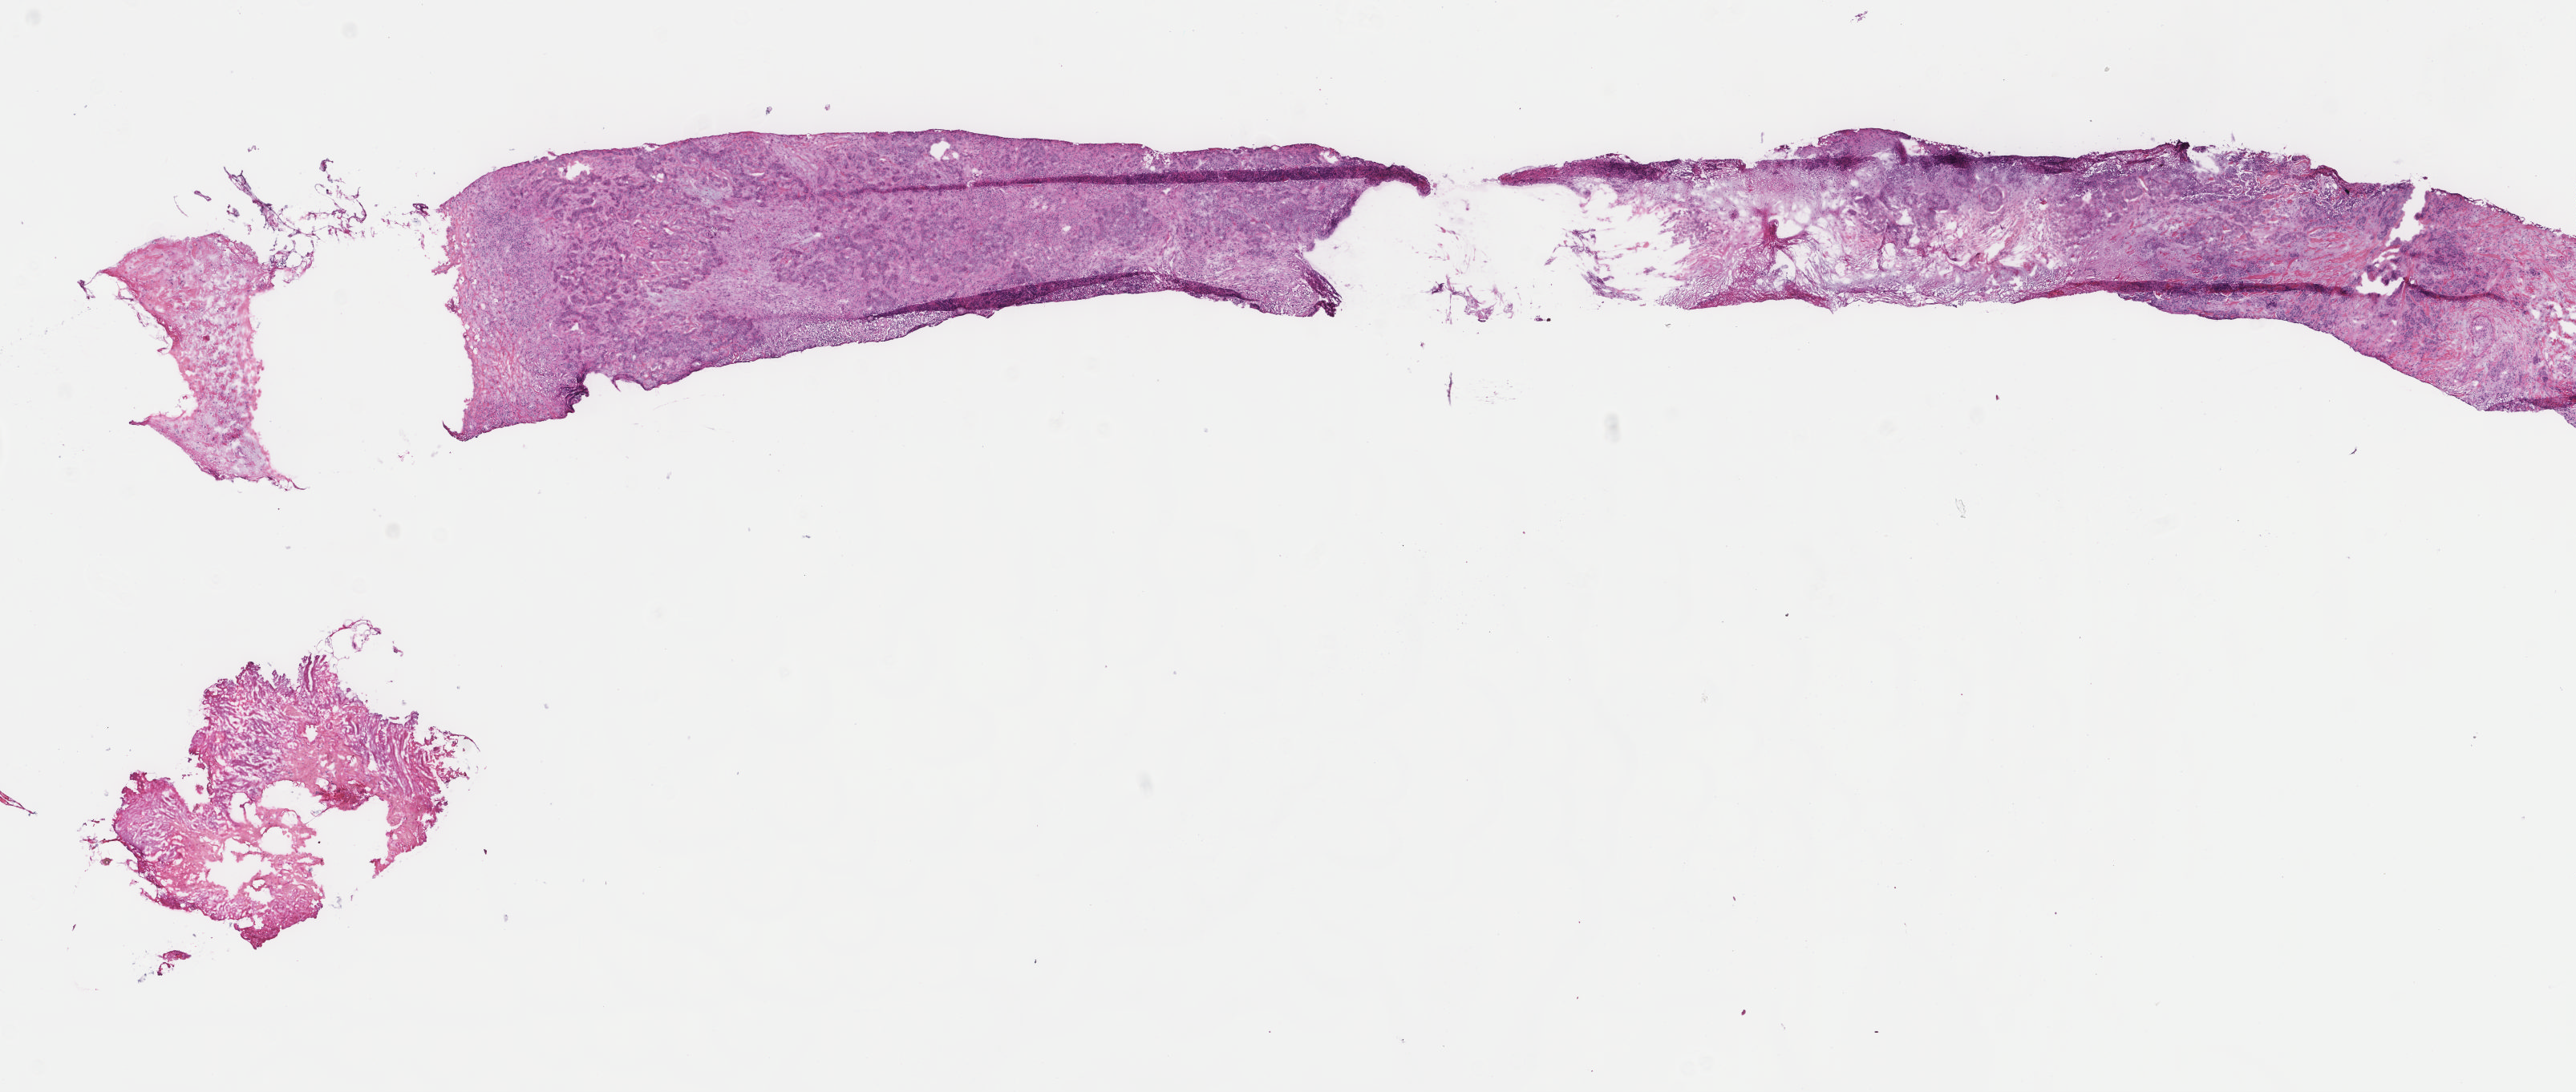
Digitized H&E-stained tissue section (whole slide), low-resolution overview of the scanned area, about 12.7 x 5.4 mm (acquisition: 40x scan), frozen section from the top of the tissue portion, breast, primary tumour sample. Patient: female, age at initial diagnosis 43 years. Composition of this section per pathologist review: tumour cells 90%, tumour nuclei 75%, normal cells 0%, stromal cells 10%, necrosis 0%. Infiltration values recorded for this section: lymphocyte infiltration 0%, monocyte infiltration 0%, neutrophil infiltration 0%.
Diagnosis: Infiltrating duct carcinoma, NOS. Laterality: left. AJCC pathologic stage: IIIA (6th edition). Lymph nodes positive (case pathology): 4 of 5 examined.